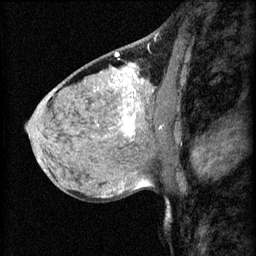
Breast MRI (dynamic contrast-enhanced), one sagittal slice. Slice 38 of 60 in the series (ordered by position). 3 images stored at this slice position (order not interpretable as contrast timing). 1.5 T. TE 4.2 ms, TR 8.2 ms. 2.2 mm slice thickness. 256 × 256 image matrix, field of view 180 × 180 mm. Female patient, age 40 years.
Outlined on this slice (semi-automatic segmentation, software-assisted and operator-edited):
- analysis volume of interest (the breast-tissue region the enhancement analysis was run in; not a lesion): bounding box <108,82,175,139> (left, top, right, bottom; pixels)
- tumour enhancement mask (voxels above the 70 % enhancement threshold inside the analysis volume of interest): <110,82,163,137>